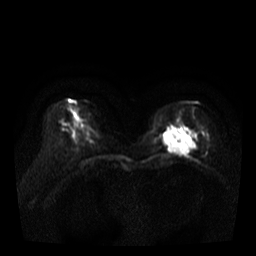
Breast MRI, one axial slice. Diffusion-weighted series; image 2 of 4 stored at this slice position (different b-values; order by instance number). 3 T. 5 mm slice thickness. 256 × 256 image matrix, field of view 320 × 320 mm. Female patient.
Annotated regions visible in this slice (expert manual segmentation):
- tumour on diffusion-weighted imaging: box from (x=165, y=131) to (x=195, y=154) px